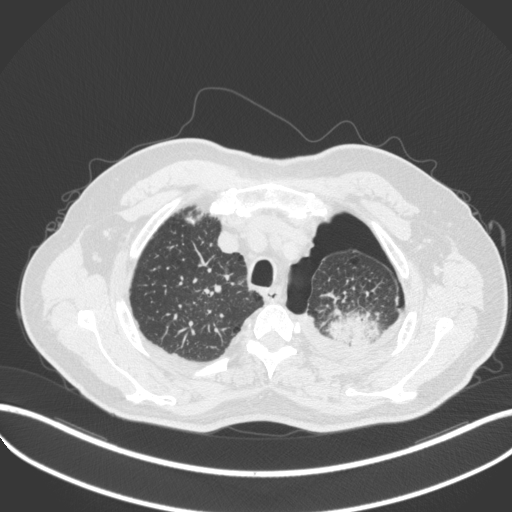
Chest CT, one axial slice; position 414 of 466 along the scan axis; 120 kVp; lung window (W 1500 / L -600 HU); 1 mm slice thickness; 512 × 512 image matrix. Male patient, age 76 years. From the clinical record (not read from this slice): clinical TNM (as recorded): T3 N0 M1b.
Structures marked on this image (bounding box drawn by a radiologist):
- lung tumour (recorded histology: adenocarcinoma): bounding box (x1, y1, x2, y2) in pixels: (328, 307, 380, 344)